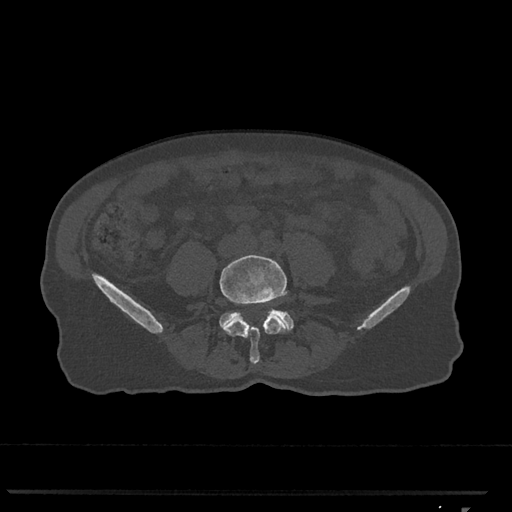
CT including the spine, one axial slice. Slice 188 of 793 in the series (ordered by position). Bone window (W 1800 / L 400 HU). 0.5 mm slice thickness. 512 × 512 image matrix, field of view 380 × 380 mm. Female patient, age 62 years. From the clinical record (not read from this slice): primary cancer: renal.
Annotated regions visible in this slice (semi-automatic segmentation, software-assisted and operator-edited):
- L4 vertebra: box from (x=219, y=255) to (x=289, y=364) px
- L5 vertebra: (x=219, y=309)–(x=294, y=330)